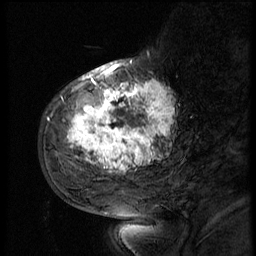
Breast MRI (dynamic contrast-enhanced), one sagittal slice. Slice 18 of 56 in the series (ordered by position). 3 images stored at this slice position (order not interpretable as contrast timing). 1.5 T. TE 4.2 ms, TR 9 ms. 2.5 mm slice thickness. 256 × 256 image matrix, field of view 180 × 180 mm. Female patient, age 51 years. Case-level facts recorded for this patient, not image findings: setting: breast cancer imaged before/during neoadjuvant chemotherapy; receptor status: triple-negative.
Outlined on this slice (semi-automatically segmented with operator editing):
- analysis volume of interest (the breast-tissue region the enhancement analysis was run in; not a lesion): bounding box [x1, y1, x2, y2] px = [52, 66, 183, 179]
- tumour enhancement mask (voxels above the 140 % enhancement threshold inside the analysis volume of interest): [67, 66, 173, 173]